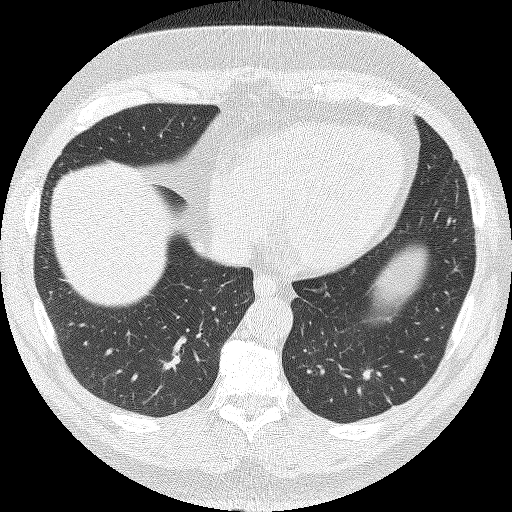
Low-dose screening chest CT, one axial slice; position 40 of 140 along the scan axis; reconstruction kernel FC51; 120 kVp; lung window (W 1500 / L -600 HU); 2 mm slice thickness; 512 × 512 image matrix.
Annotated regions visible in this slice (expert manual segmentation):
- lesion 1 (tumor, lower lobe of left lung): bounding box <362,369,378,380> (left, top, right, bottom; pixels)